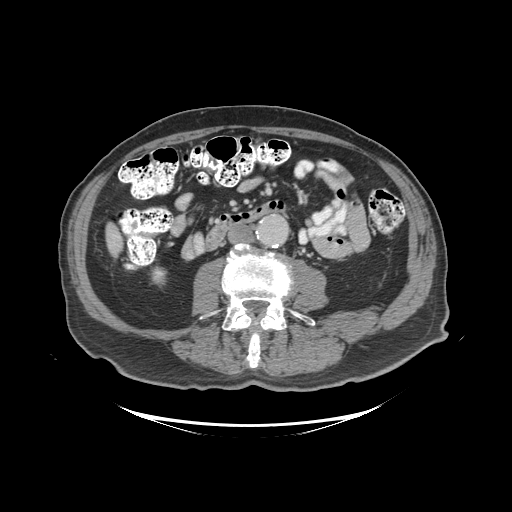
Contrast-enhanced abdominal CT (liver protocol), one axial slice; slice 22 of 99 in the series (ordered by position); 140 kVp; soft-tissue window (W 400 / L 40 HU); 2.5 mm slice thickness; 512 × 512 image matrix, field of view 460 × 460 mm. Case-level facts recorded for this patient, not image findings: diagnosis: hepatocellular carcinoma (patient treated with transarterial chemoembolisation; whether this scan precedes or follows treatment is not stated here); TNM stage (as recorded): Stage-I; Child-Pugh class: A; tumour differentiation: moderately differentiated.
Structures marked on this image (semi-automatically segmented with operator editing):
- liver parenchyma outside the tumour (the mass and vessels are separate outlines, so this box may not span the whole liver): box from (x=106, y=224) to (x=122, y=255) px